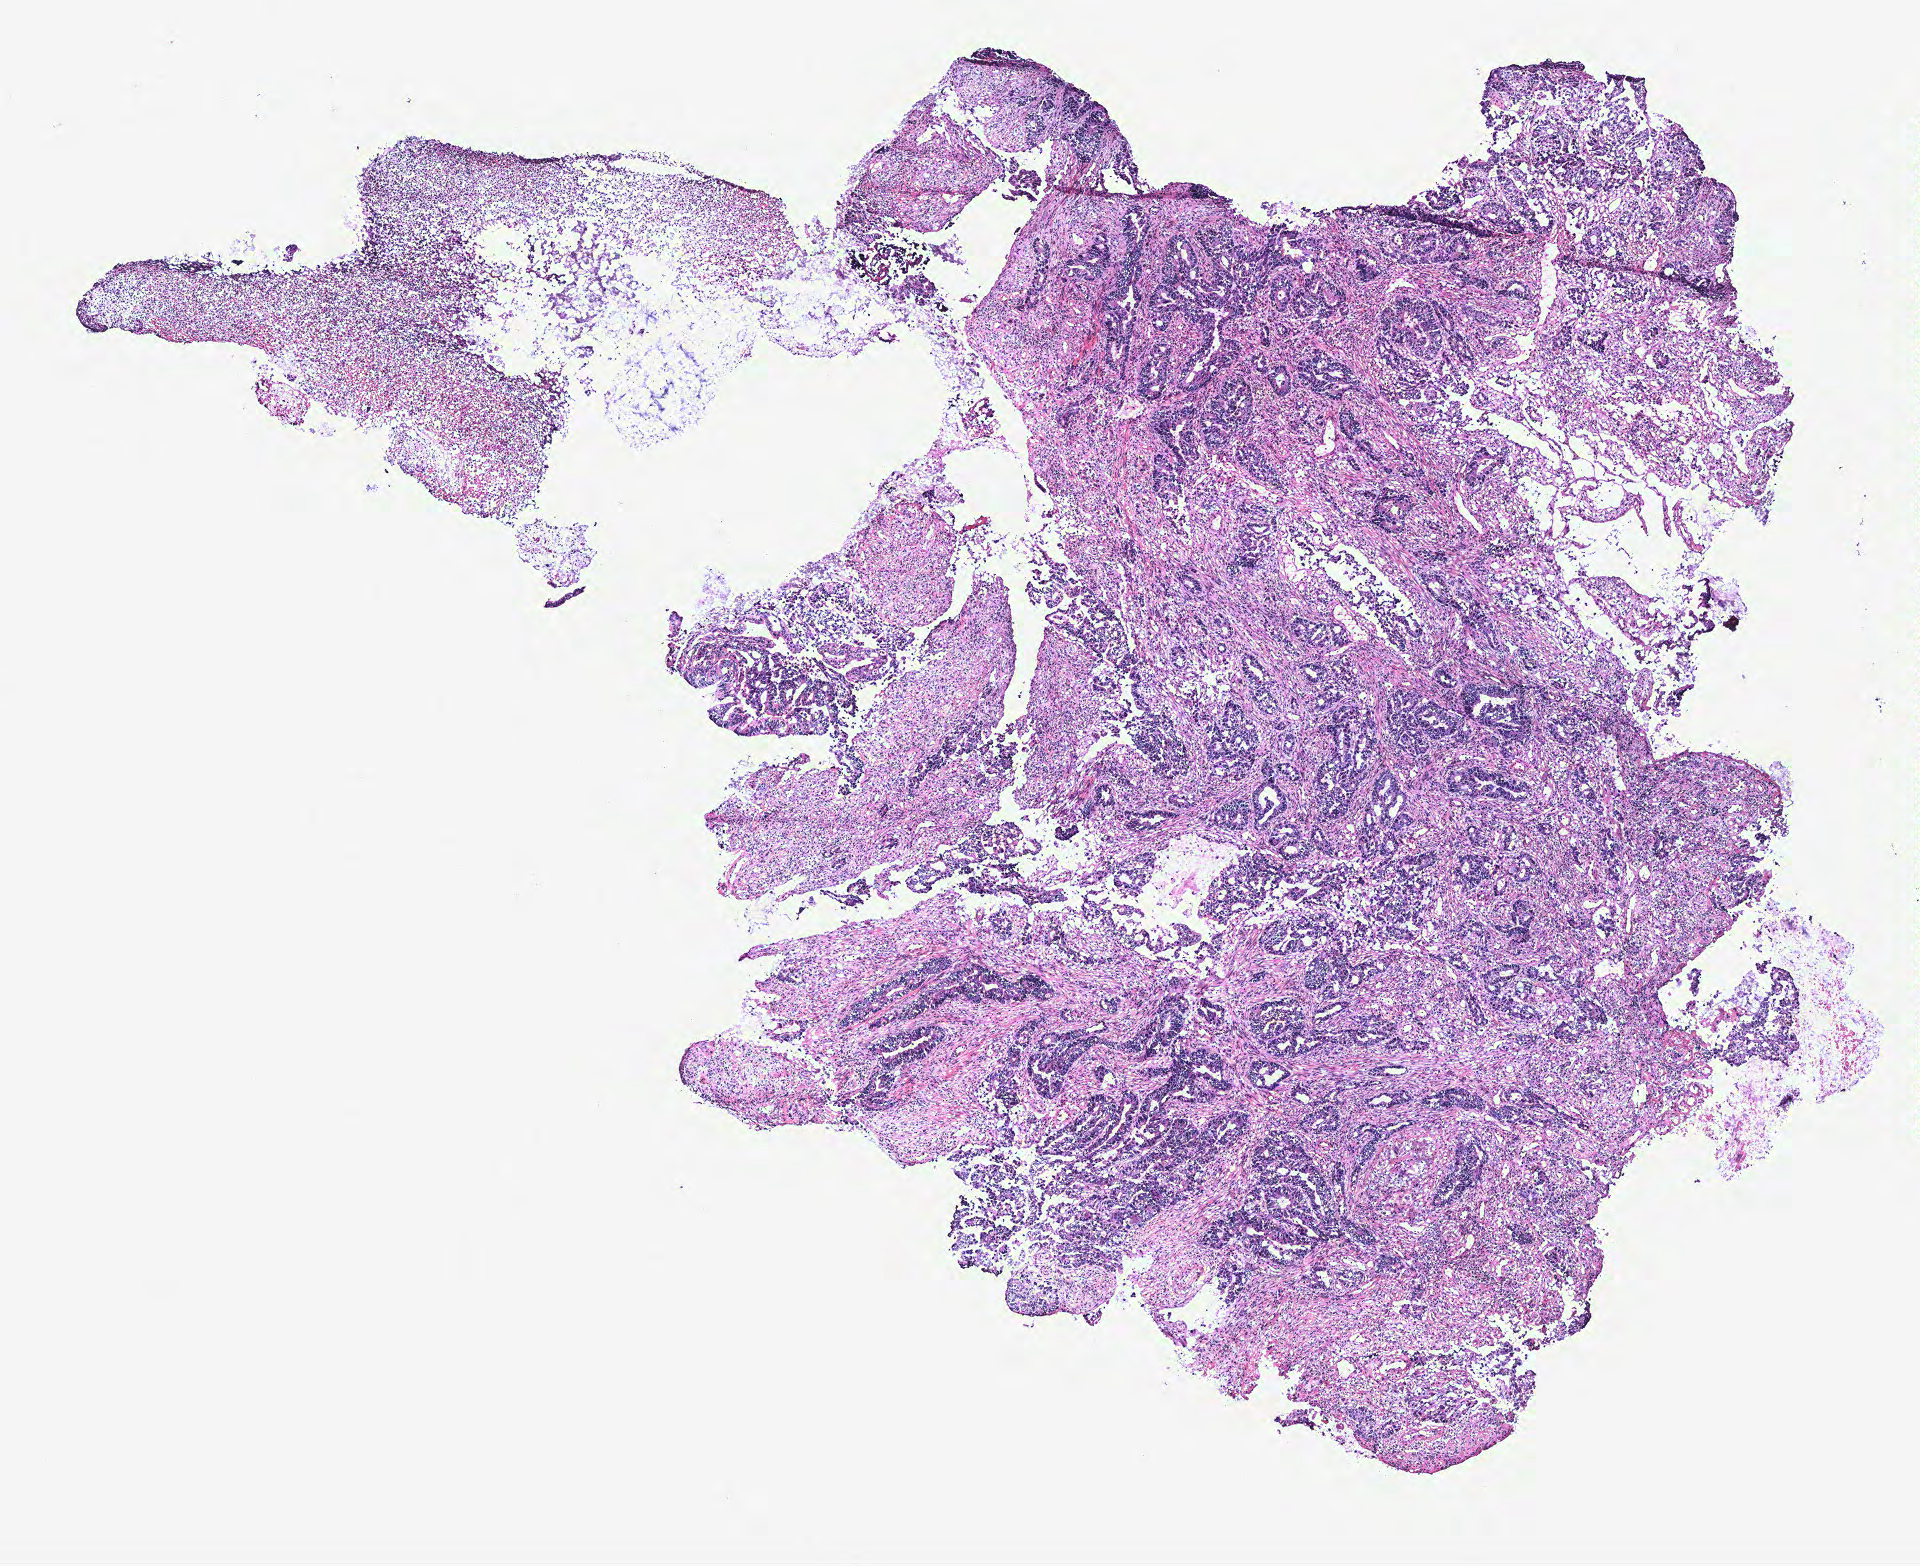
Digitized H&E-stained tissue section (whole slide), whole scanned area (about 7.7 x 6.3 mm, acquisition: 40x scan) shown as a low-resolution overview, colon, tissue type not recorded.
* patient diagnosis (cohort enrolment): colon cancer (colon)